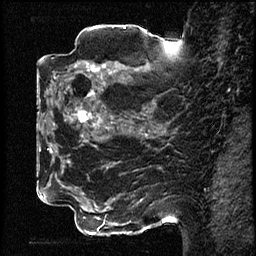
Breast MRI (dynamic contrast-enhanced), one sagittal slice. Slice 34 of 78 in the series (ordered by position). Dynamic contrast-enhanced study with each time point stored as its own series, time point 2 of 3 at this slice position (early post-contrast, ordered by acquisition time). 1.5 T. TE 4.2 ms, TR 17.6 ms. 256 × 256 image matrix. Female patient, age 42 years. Case-level facts recorded for this patient, not image findings: setting: breast cancer imaged before/during neoadjuvant chemotherapy; receptor status: HER2-positive.
Outlined on this slice (semi-automatic segmentation, software-assisted and operator-edited):
- analysis volume of interest (the breast-tissue region the enhancement analysis was run in; not a lesion): bounding box <50,48,131,129> (left, top, right, bottom; pixels)
- tumour enhancement mask (voxels above the 100 % enhancement threshold inside the analysis volume of interest): <77,63,100,122>